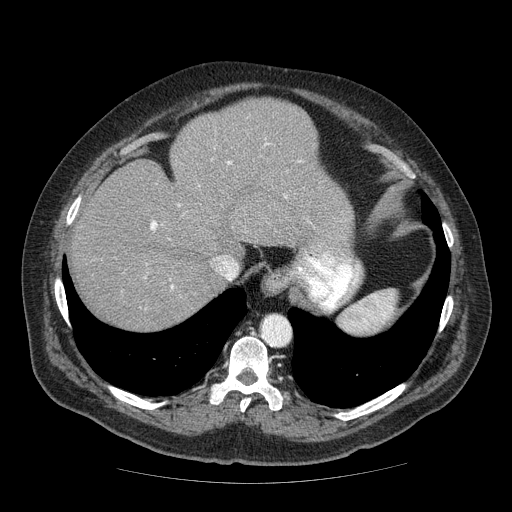
Contrast-enhanced abdominal CT (liver protocol), one axial slice. Slice 53 of 85 in the series (ordered by position). Reconstruction kernel STANDARD. 120 kVp. Soft-tissue window (W 400 / L 40 HU). 2.5 mm slice thickness. 512 × 512 image matrix, field of view 420 × 420 mm. Case-level facts recorded for this patient, not image findings: diagnosis: hepatocellular carcinoma (patient treated with transarterial chemoembolisation; whether this scan precedes or follows treatment is not stated here); TNM stage (as recorded): Stage-IIIA; Child-Pugh class: A; tumour size: 7 cm.
Annotated regions visible in this slice (semi-automatically segmented with operator editing):
- abdominal aorta: box from (x=261, y=316) to (x=290, y=346) px
- liver parenchyma outside the tumour (the mass and vessels are separate outlines, so this box may not span the whole liver): (x=70, y=98)–(x=352, y=330)
- liver vessels: (x=150, y=143)–(x=287, y=289)